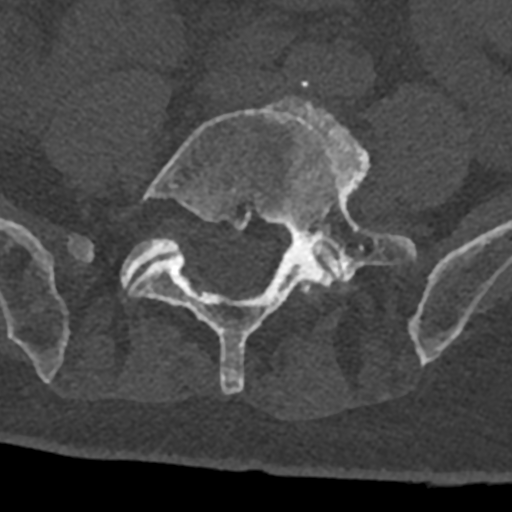
CT including the spine, one axial slice; position 200 of 797 along the scan axis; 120 kVp; bone window (W 1800 / L 400 HU); 0.5 mm slice thickness; 512 × 512 image matrix, field of view 160 × 160 mm. Patient: male, 74 years. Case-level facts recorded for this patient, not image findings: primary cancer: renal; vertebrae with lytic lesions (as recorded): T10, L1, L2, L3, L4, L5.
Structures marked on this image (semi-automatically segmented with operator editing):
- L4 vertebra: box from (x=292, y=279) to (x=313, y=296) px
- L5 vertebra: (x=129, y=96)–(x=417, y=394)